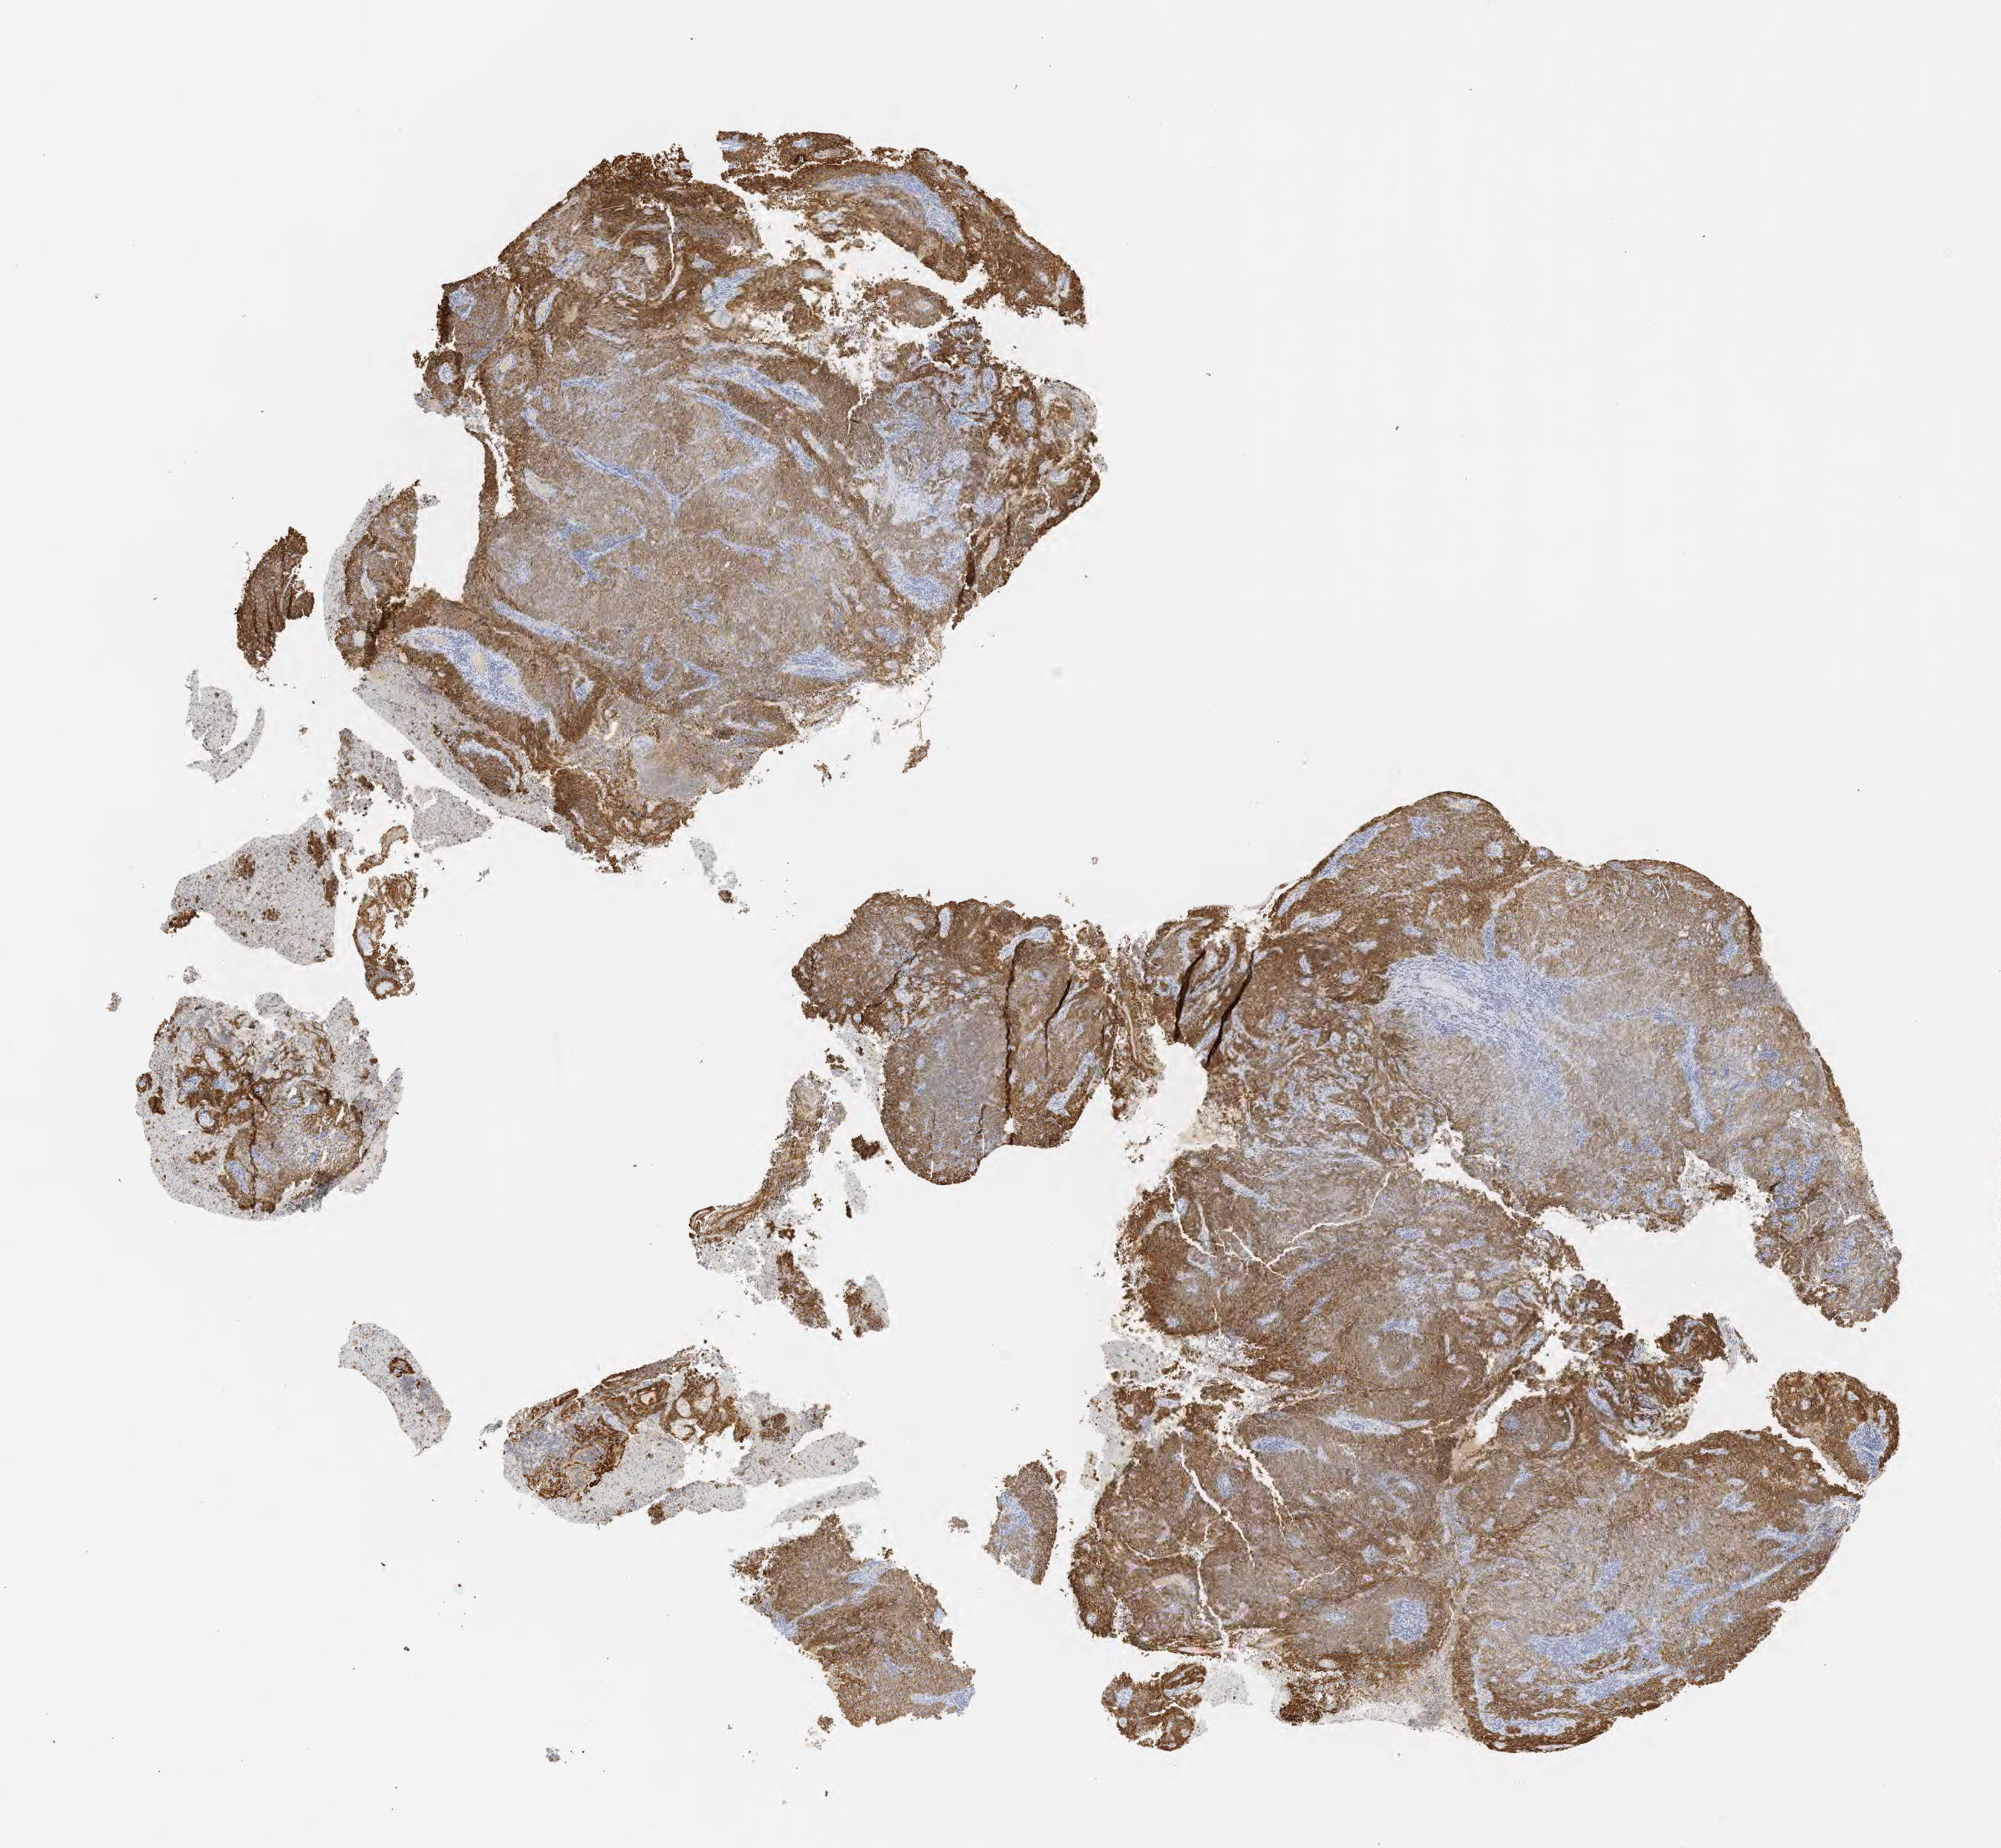
IHC for Ber-EP4, whole-slide image — shown as a low-resolution overview of the whole scanned area (about 10.6 x 9.8 mm). Specimen: tumor tissue. Site: cervix. Female patient, 70 years old.
Histologic diagnosis: Squamous cell carcinoma, large cell, nonkeratinizing, NOS.